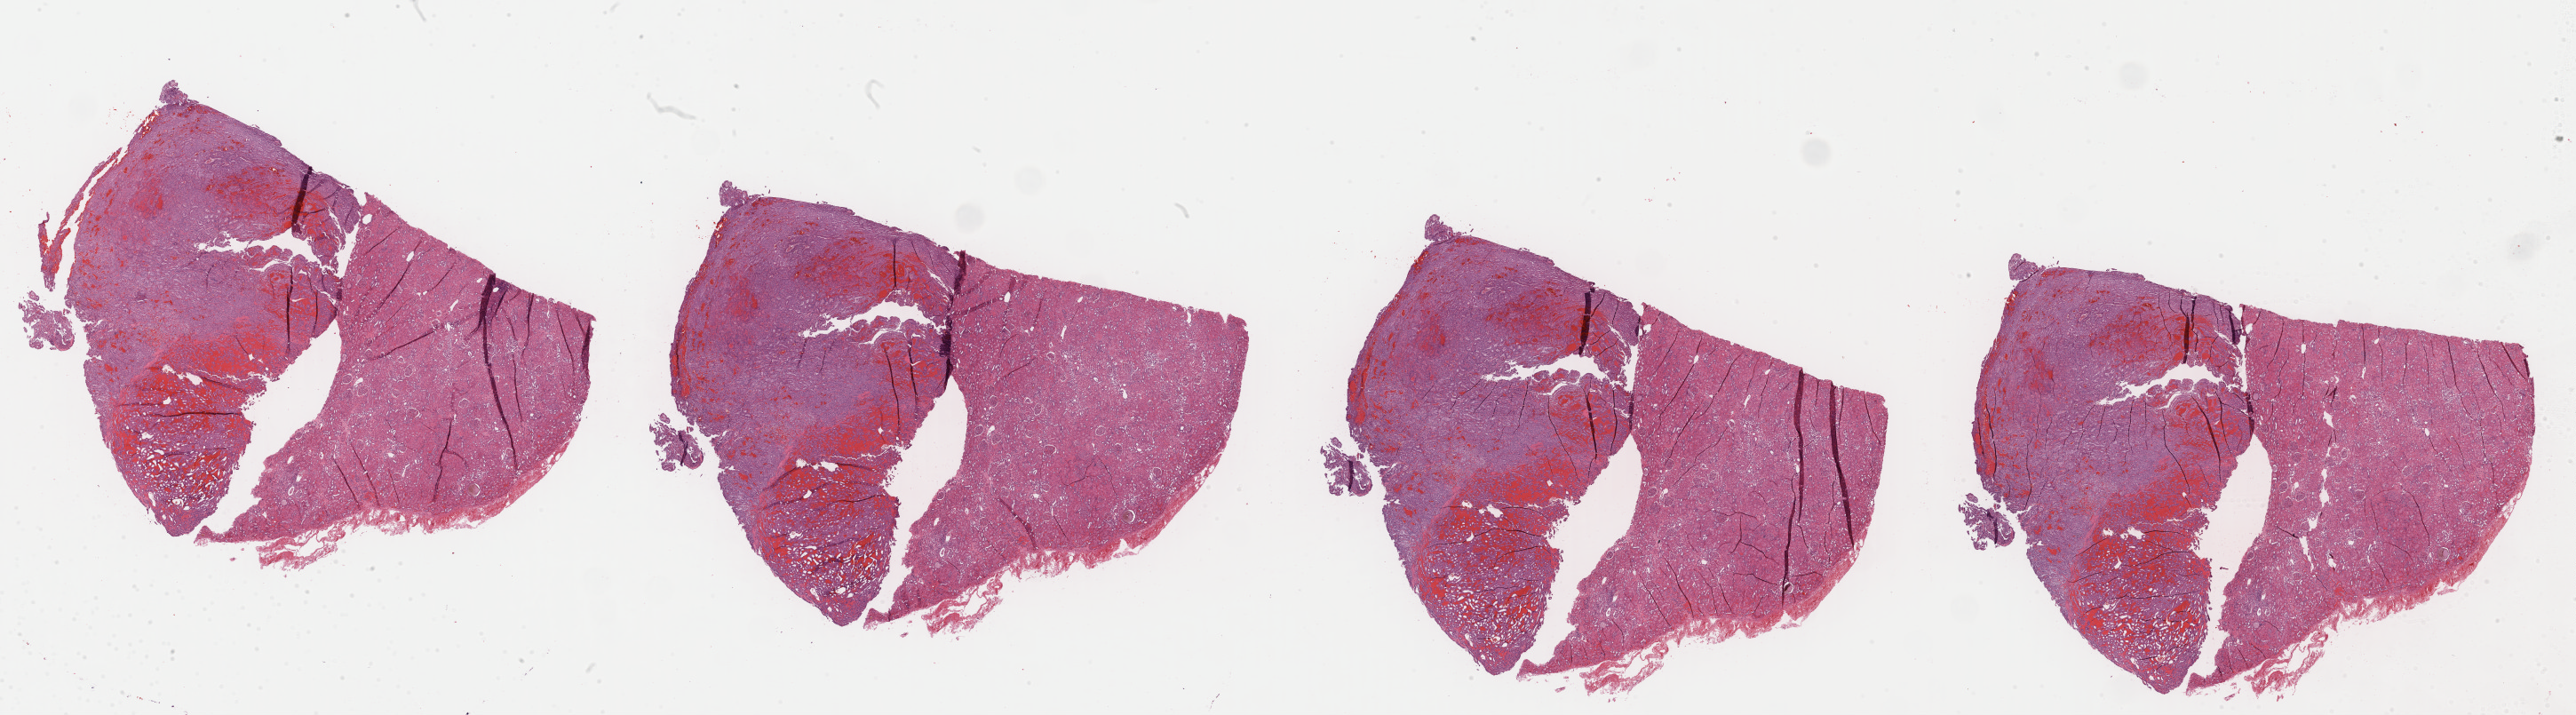
Whole-slide histology image, H&E, a low-resolution overview of the entire scanned area, about 45.8 x 12.7 mm, formalin-fixed paraffin-embedded (FFPE) diagnostic section, kidney, primary tumour sample. Patient: male, age at initial diagnosis 66 years.
* diagnosis: Papillary adenocarcinoma, NOS
* AJCC pathologic stage: I (7th edition)
* laterality: right